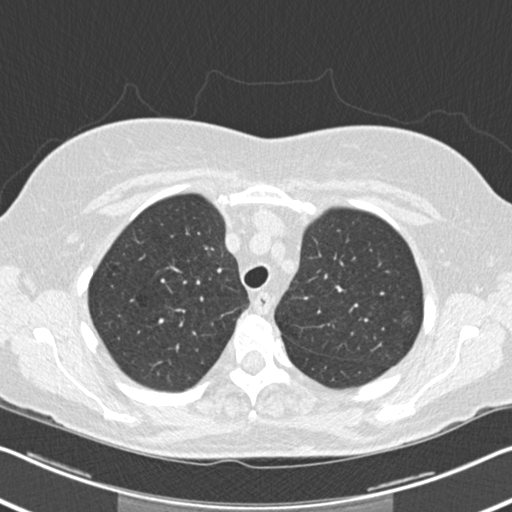
Chest CT (low-dose screening protocol), one axial image; second screening round (one year after baseline); lung window (W 1500 / L -600 HU); 2 mm slice thickness; standard (soft-tissue) reconstruction kernel (B30f). Female, age 60 years at enrolment. Current smoker at enrolment.
Expert-annotated lung lesion, bounding box [x1, y1, x2, y2] px = [387, 305, 424, 342]. The screening reader recorded 6 non-calcified nodules or masses ≥4 mm on this exam (right upper lobe, right middle lobe, right lower lobe, right lower lobe, left lower lobe, lingula); which of them this box marks is not recorded. Lung cancer was diagnosed 495 days after this screen (after the third annual screen): non-small cell carcinoma, left upper lobe, poorly differentiated (G3), stage IB (AJCC 6th edition), 7 mm at pathology.